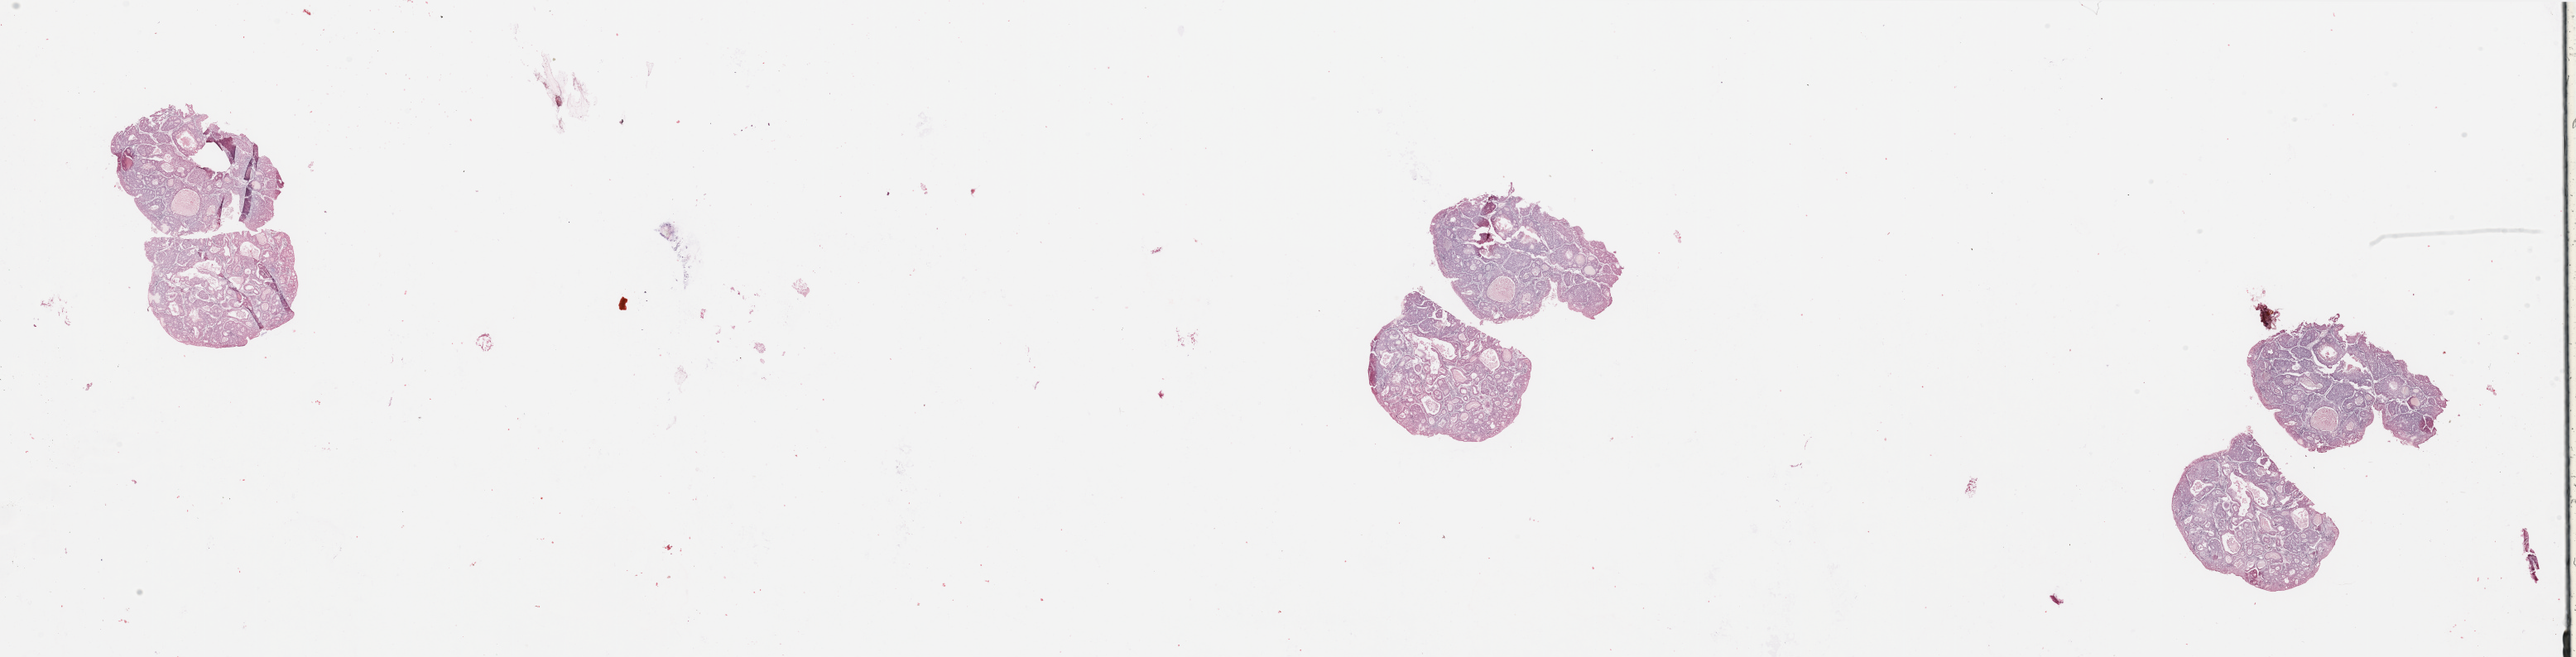
Whole-slide histology image, H&E-stained, whole scanned area (about 49.2 x 12.6 mm) shown as a low-resolution overview. Tumour tissue sample, sampled site: uterus. Female, 65 y/o. Histologic grade: G2 (moderately differentiated). Composition of this section per pathologist review: tumour nuclei 80%, necrosis 10%.
- AJCC pathologic stage: III
- primary tumour site (as recorded): anterior endometrium
- histologic diagnosis: Endometrioid adenocarcinoma, NOS